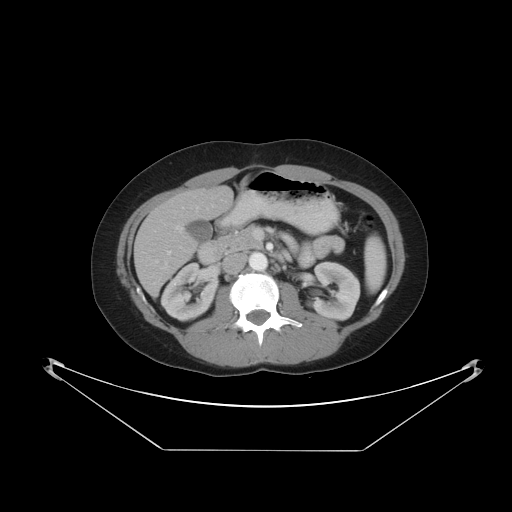
Contrast-enhanced abdominal CT, one axial slice; slice 20 of 48 in the series (ordered by position); 120 kVp; soft-tissue window (W 400 / L 40 HU); 512 × 512 image matrix, field of view 482 × 482 mm. Female patient, age 38 years. From the clinical record (not read from this slice): diagnosis: colorectal cancer liver metastases, imaged before liver resection; multiple liver metastases: yes; largest metastasis: 2.5 cm; chemotherapy before resection: no.
Outlined on this slice (outlined manually by an expert reader):
- hepatic veins: bounding box [x1, y1, x2, y2] px = [175, 207, 197, 232]
- liver: [136, 188, 233, 294]
- planned liver remnant (the part of the liver to remain after resection): [170, 188, 232, 220]
- portal vein (with intrahepatic branches): [156, 205, 213, 262]